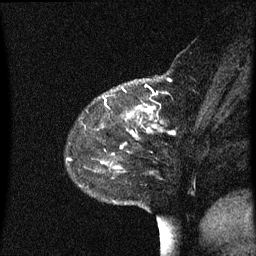
Breast MRI (dynamic contrast-enhanced), one sagittal slice. Slice 17 of 60 in the series (ordered by position). Dynamic contrast-enhanced series, image 2 of 3 at this slice position (ordered by acquisition). 1.5 T. TE 4.2 ms, TR 8.4 ms. 2 mm slice thickness. 256 × 256 image matrix, field of view 200 × 200 mm. Patient: female, 48 years. From the clinical record (not read from this slice): setting: breast cancer imaged before/during neoadjuvant chemotherapy; receptor status: HR-positive, HER2-negative.
Structures marked on this image (semi-automatically segmented with operator editing):
- analysis volume of interest (the breast-tissue region the enhancement analysis was run in; not a lesion): bounding box <92,81,195,221> (left, top, right, bottom; pixels)
- tumour enhancement mask (voxels above the 70 % enhancement threshold inside the analysis volume of interest): <106,100,155,128>